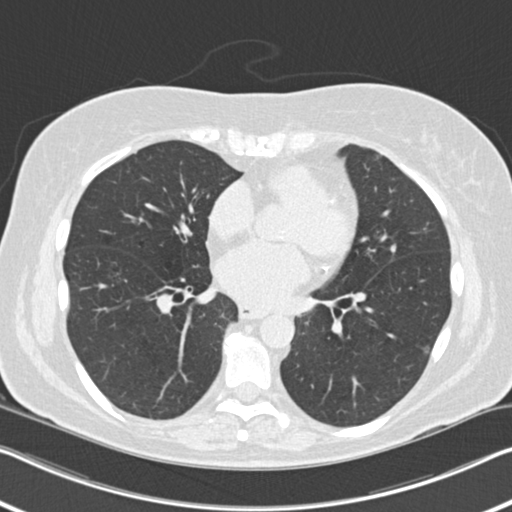
Low-dose screening chest CT, axial slice. Second annual screen. Lung window (W 1500 / L -600 HU). 2 mm slice thickness. Standard (soft-tissue) reconstruction kernel (B30f). Female participant, aged 60 years at enrolment.
Expert-annotated lung lesion, box from (x=376, y=238) to (x=409, y=268) px. The screening reader recorded 6 non-calcified nodules or masses ≥4 mm on this exam (right upper lobe, right middle lobe, right lower lobe, right lower lobe, left lower lobe, lingula); which of them this box marks is not recorded. Later outcome: lung cancer diagnosed 495 days after this screen (after the third annual screen) — non-small cell carcinoma, left upper lobe, poorly differentiated (G3), stage IB (AJCC 6th edition), 7 mm at pathology.